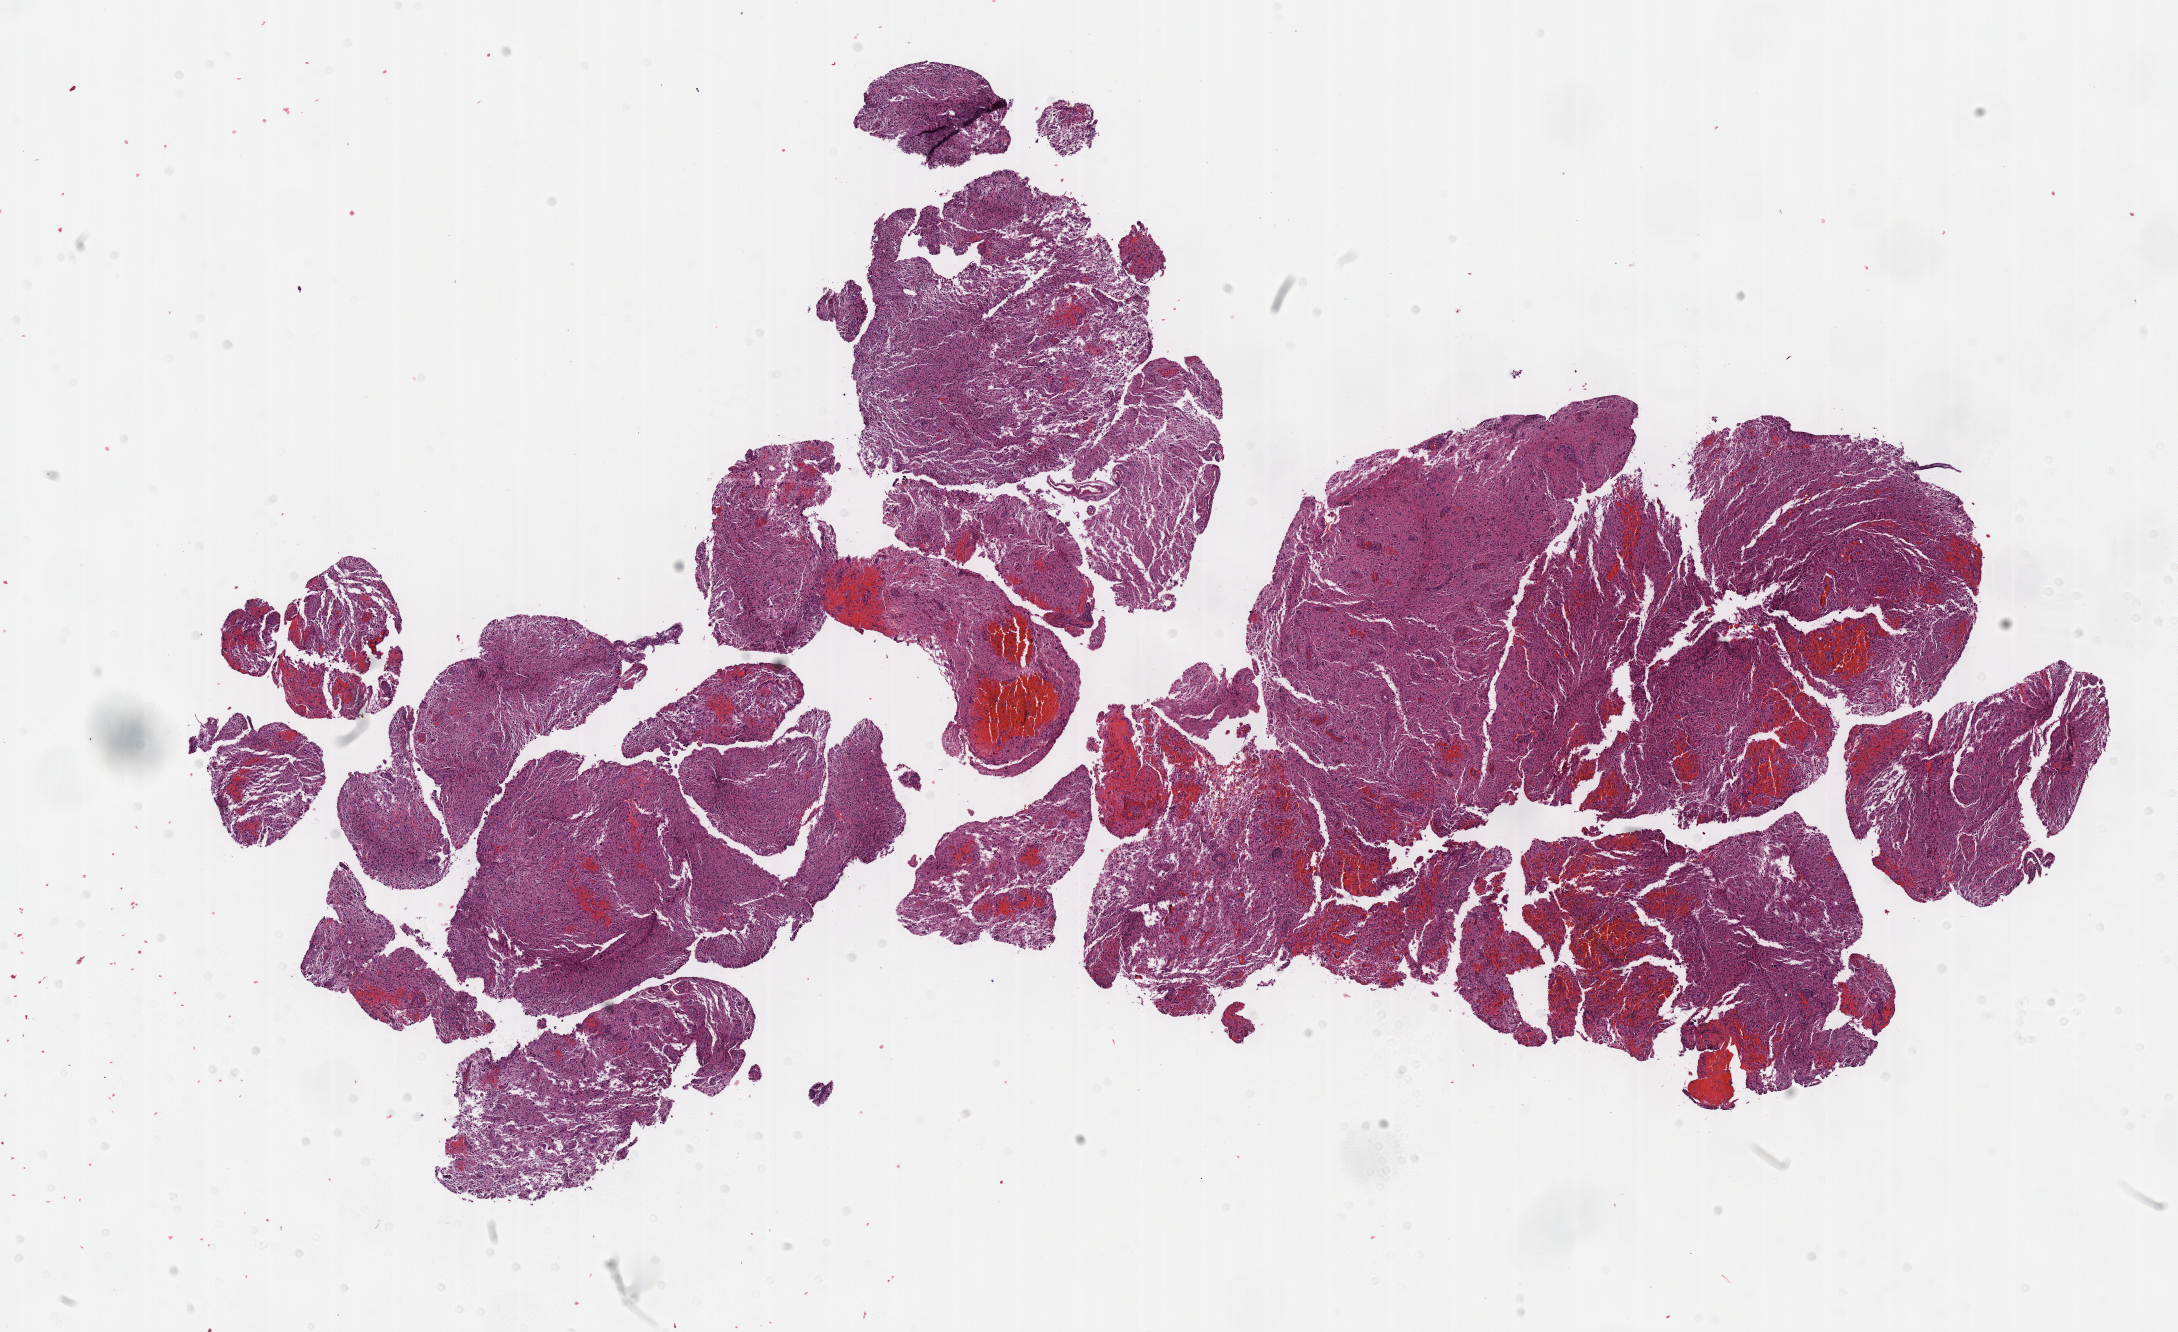
H&E whole-slide image — whole scanned area (about 17.6 x 10.8 mm, acquisition: 40x scan) shown as a low-resolution overview; FFPE section; primary tumour sample from the brain. Female patient; age at initial diagnosis 24 years. Histologic grade: G3 (poorly differentiated).
• histologic diagnosis: Astrocytoma, anaplastic (cerebrum)